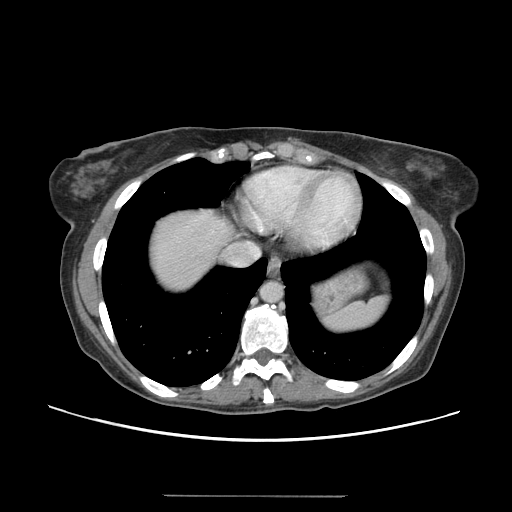
Contrast-enhanced abdominal CT, one axial slice. Slice 132 of 144 in the series (ordered by position). 120 kVp. Intravenous contrast given. Soft-tissue window (W 400 / L 40 HU). 2.5 mm slice thickness. 512 × 512 image matrix. Female patient, age 53 years. From the clinical record (not read from this slice): diagnosis: colorectal cancer liver metastases, imaged before liver resection; multiple liver metastases: yes; largest metastasis: 1.1 cm.
Annotated regions visible in this slice (outlined manually by an expert reader):
- hepatic veins: box from (x=253, y=248) to (x=260, y=257) px
- liver: (x=147, y=209)–(x=230, y=294)
- planned liver remnant (the part of the liver to remain after resection): (x=147, y=208)–(x=229, y=285)